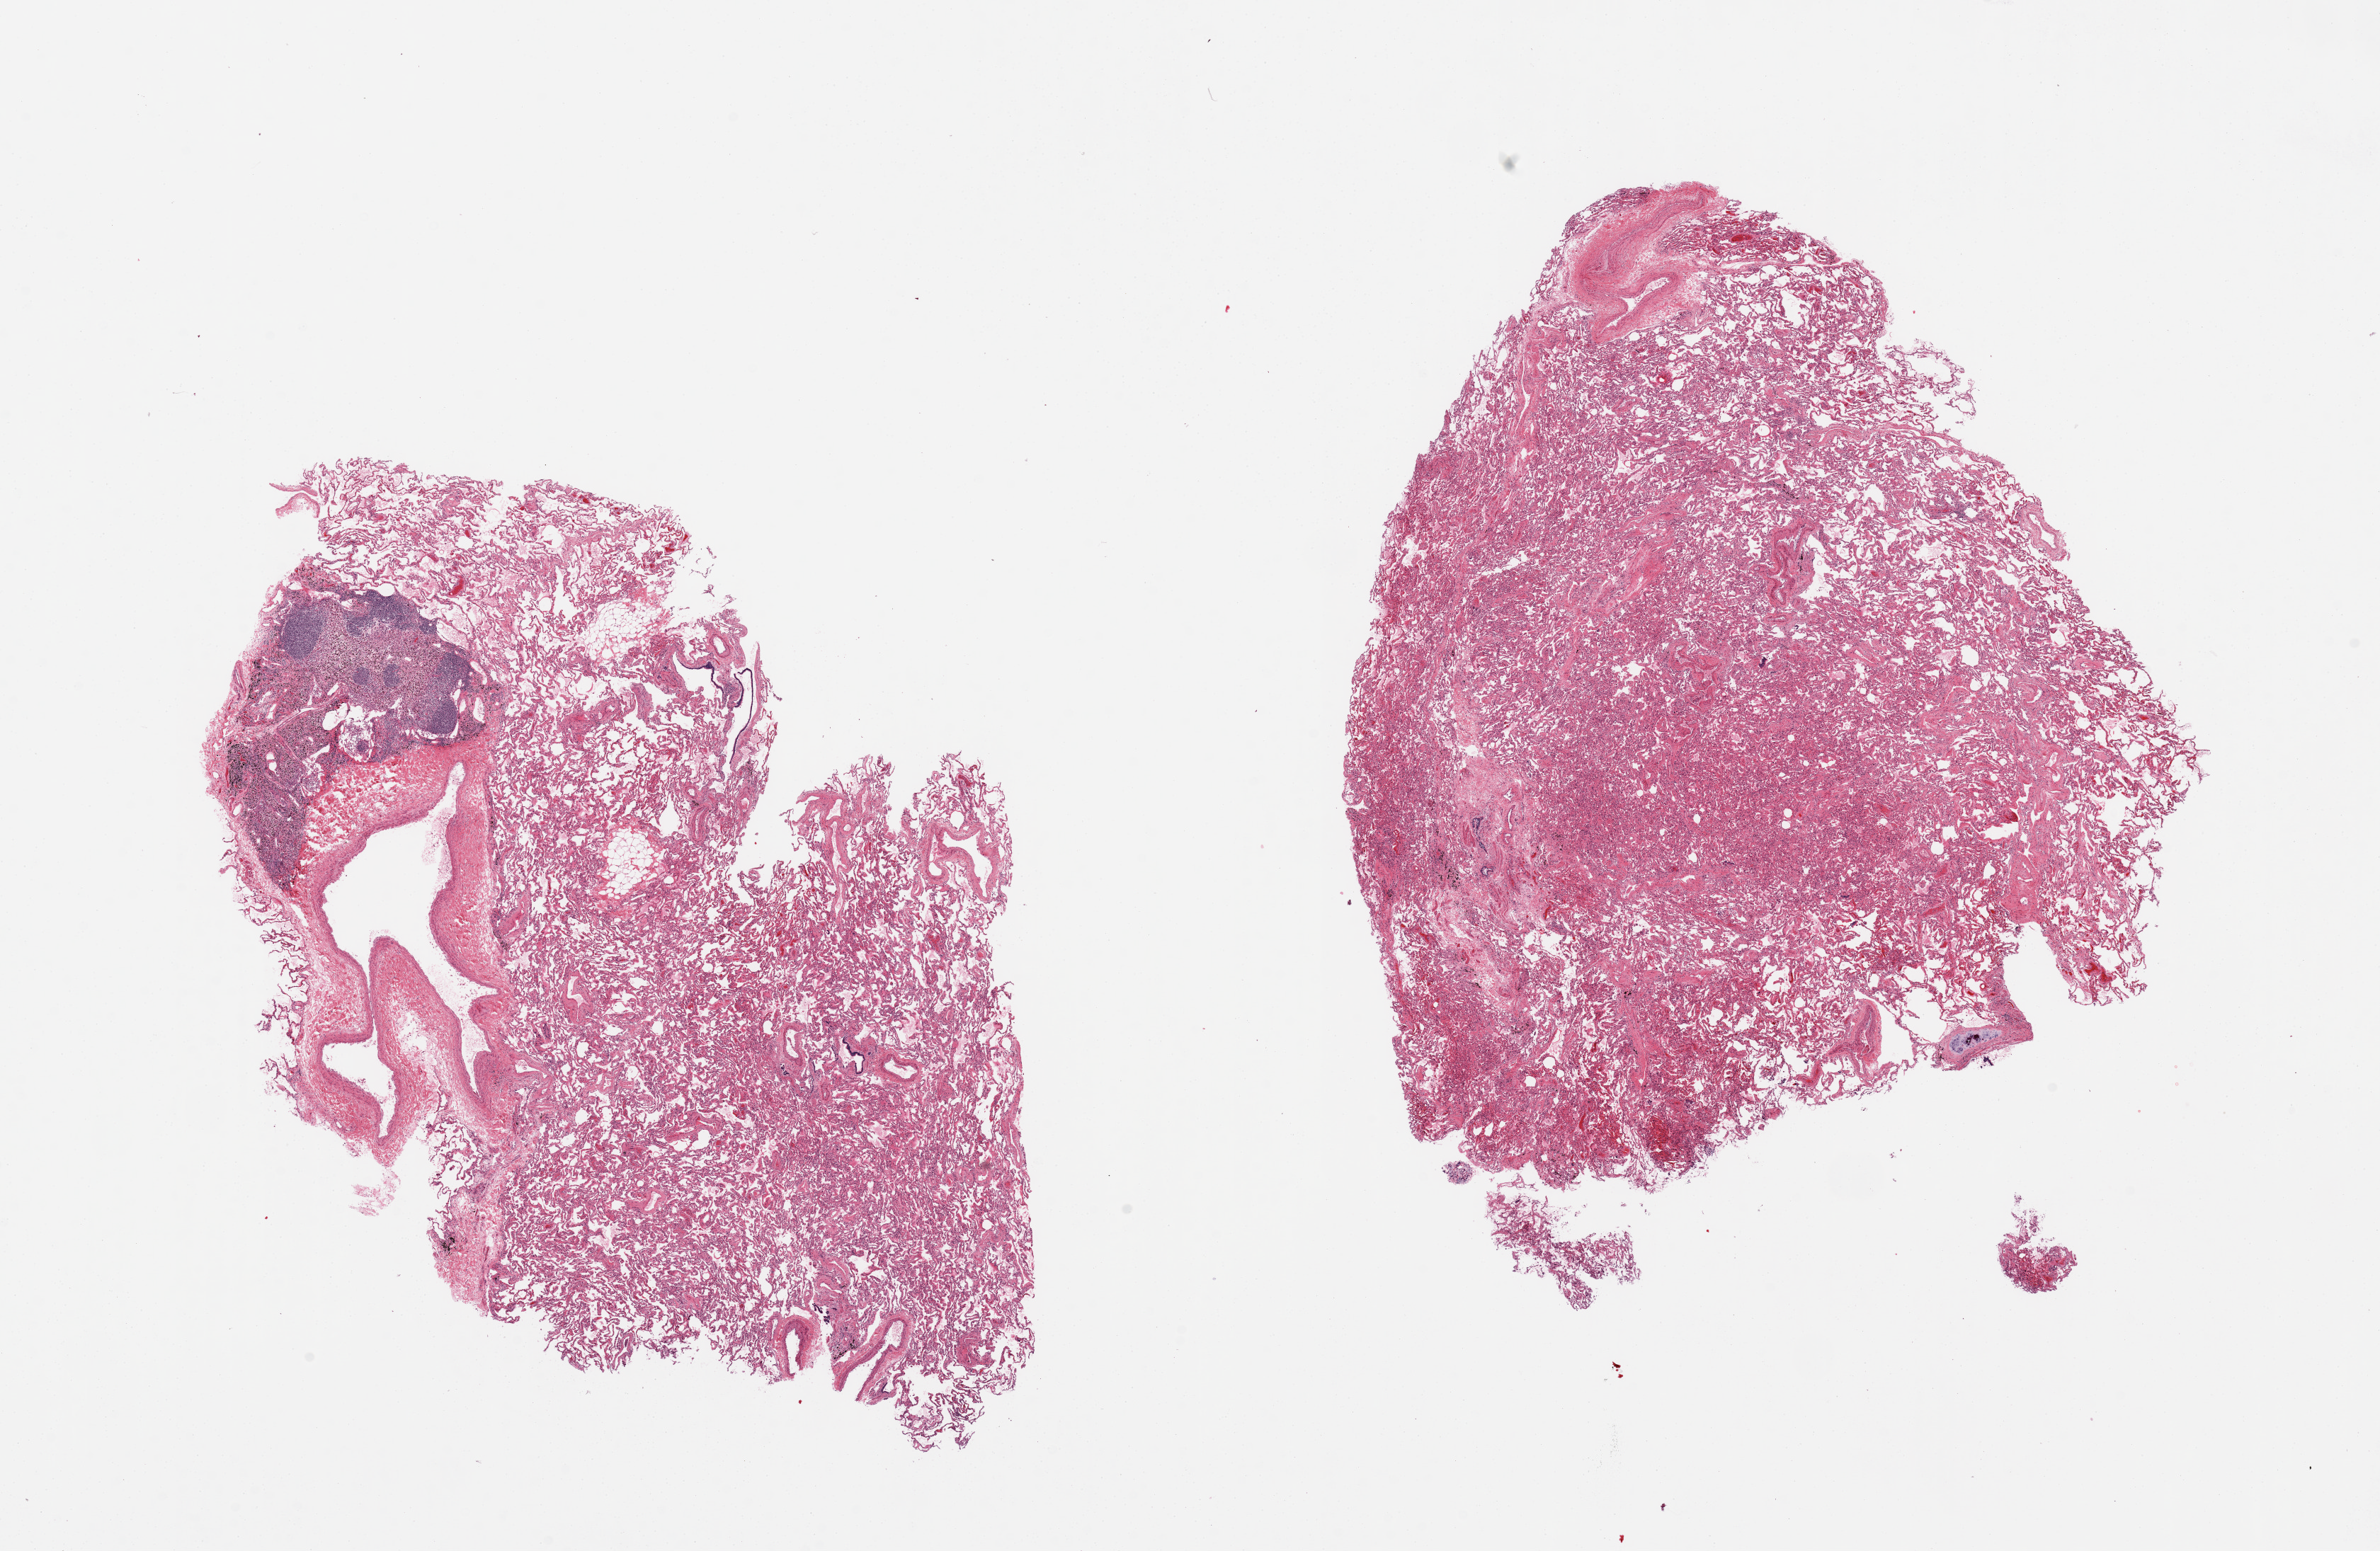
Digitized hematoxylin and eosin (H&E)-stained section — whole scanned area (about 26.6 x 17.3 mm, slide scanned at 20x) shown as a low-resolution overview, PAXgene-fixed paraffin-embedded (PFPE) section, target tissue: lung, tissue donor sample. Donor: male.
Pathologist's review note for this sample: 2 pieces, intrapulmonary lymph node, includes several large vessels and focus of cartilage, some hemosiderin-laden macrophages.